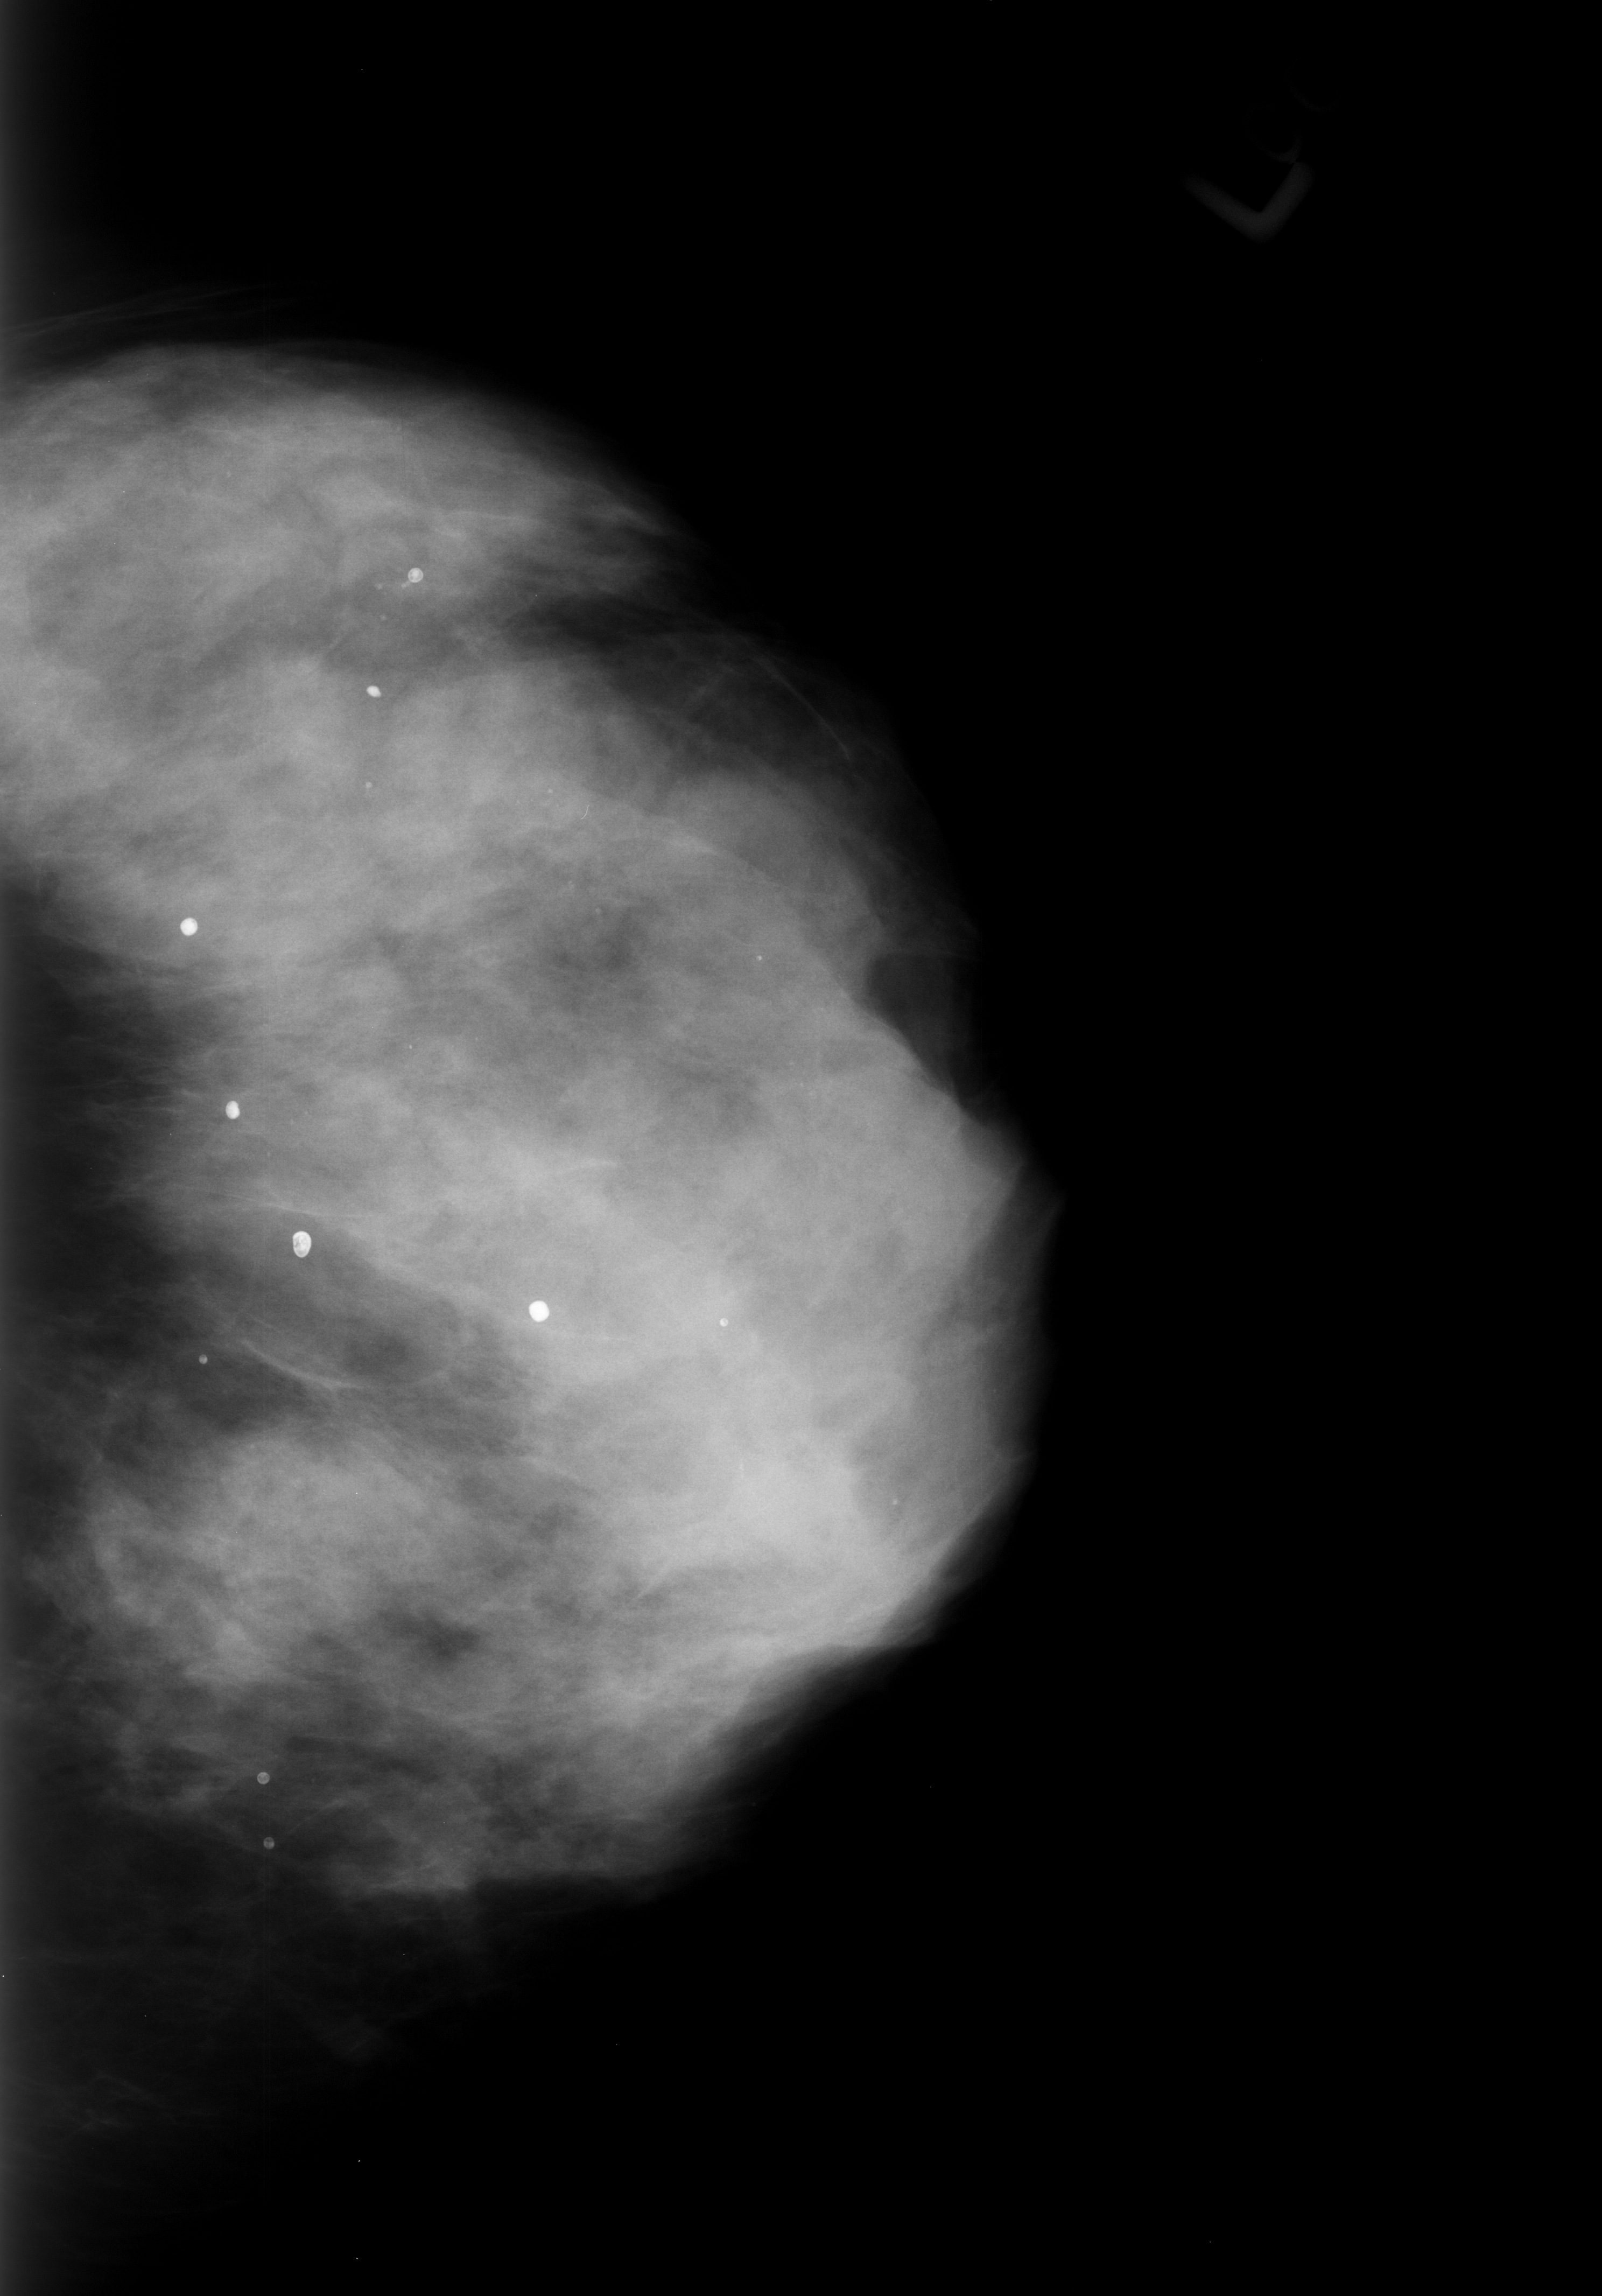
Digitized screen-film mammogram, left breast, CC view, breast composition: extremely dense (BI-RADS density category 4 of 4).
- Abnormality record for this image: Finding 1 of 6: calcifications, morphology round and regular / lucent center / punctate, distribution diffusely scattered; BI-RADS assessment category 2; benign; no additional work-up was recommended (benign without callback).
- Finding 2 of 6: calcifications, morphology round and regular / lucent center / punctate, distribution diffusely scattered; BI-RADS assessment category 2; benign without callback (not worked up further).
- Finding 3 of 6: calcifications, morphology round and regular / lucent center / punctate, distribution diffusely scattered; BI-RADS assessment category 2; subtlety rating 5 on a 1 (subtle) to 5 (obvious) scale; benign; no additional work-up was recommended (benign without callback).
- Finding 4 of 6: calcifications, morphology round and regular / lucent center / punctate, distribution diffusely scattered; BI-RADS assessment category 2; subtlety rating 5 on a 1 (subtle) to 5 (obvious) scale; benign without callback (not worked up further).
- Finding 5 of 6: calcifications, morphology round and regular / lucent center / punctate, distribution diffusely scattered; BI-RADS assessment category 2; benign; no additional work-up was recommended (benign without callback).
- Finding 6 of 6: calcifications, morphology round and regular / lucent center / punctate, distribution diffusely scattered; BI-RADS assessment category 2; benign without callback (not worked up further).